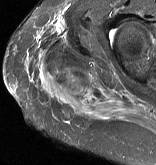
MRI of an extremity soft-tissue mass, one axial slice. Position 43 of 57 along the scan axis. STIR. MR volume resampled by the dataset authors to the PET/CT grid (not the native acquisition matrix). 3.27 mm slice thickness. 156 × 165 image matrix, field of view 152 × 161 mm. Female patient. From the clinical record (not read from this slice): histological type: epithelioid sarcoma with vascular differentiation; site of the primary tumour: right buttock.
Annotated regions visible in this slice (expert contour drawn on MRI and transferred to this co-registered scan by the dataset authors):
- gross tumour volume (mass): box from (x=44, y=60) to (x=91, y=90) px